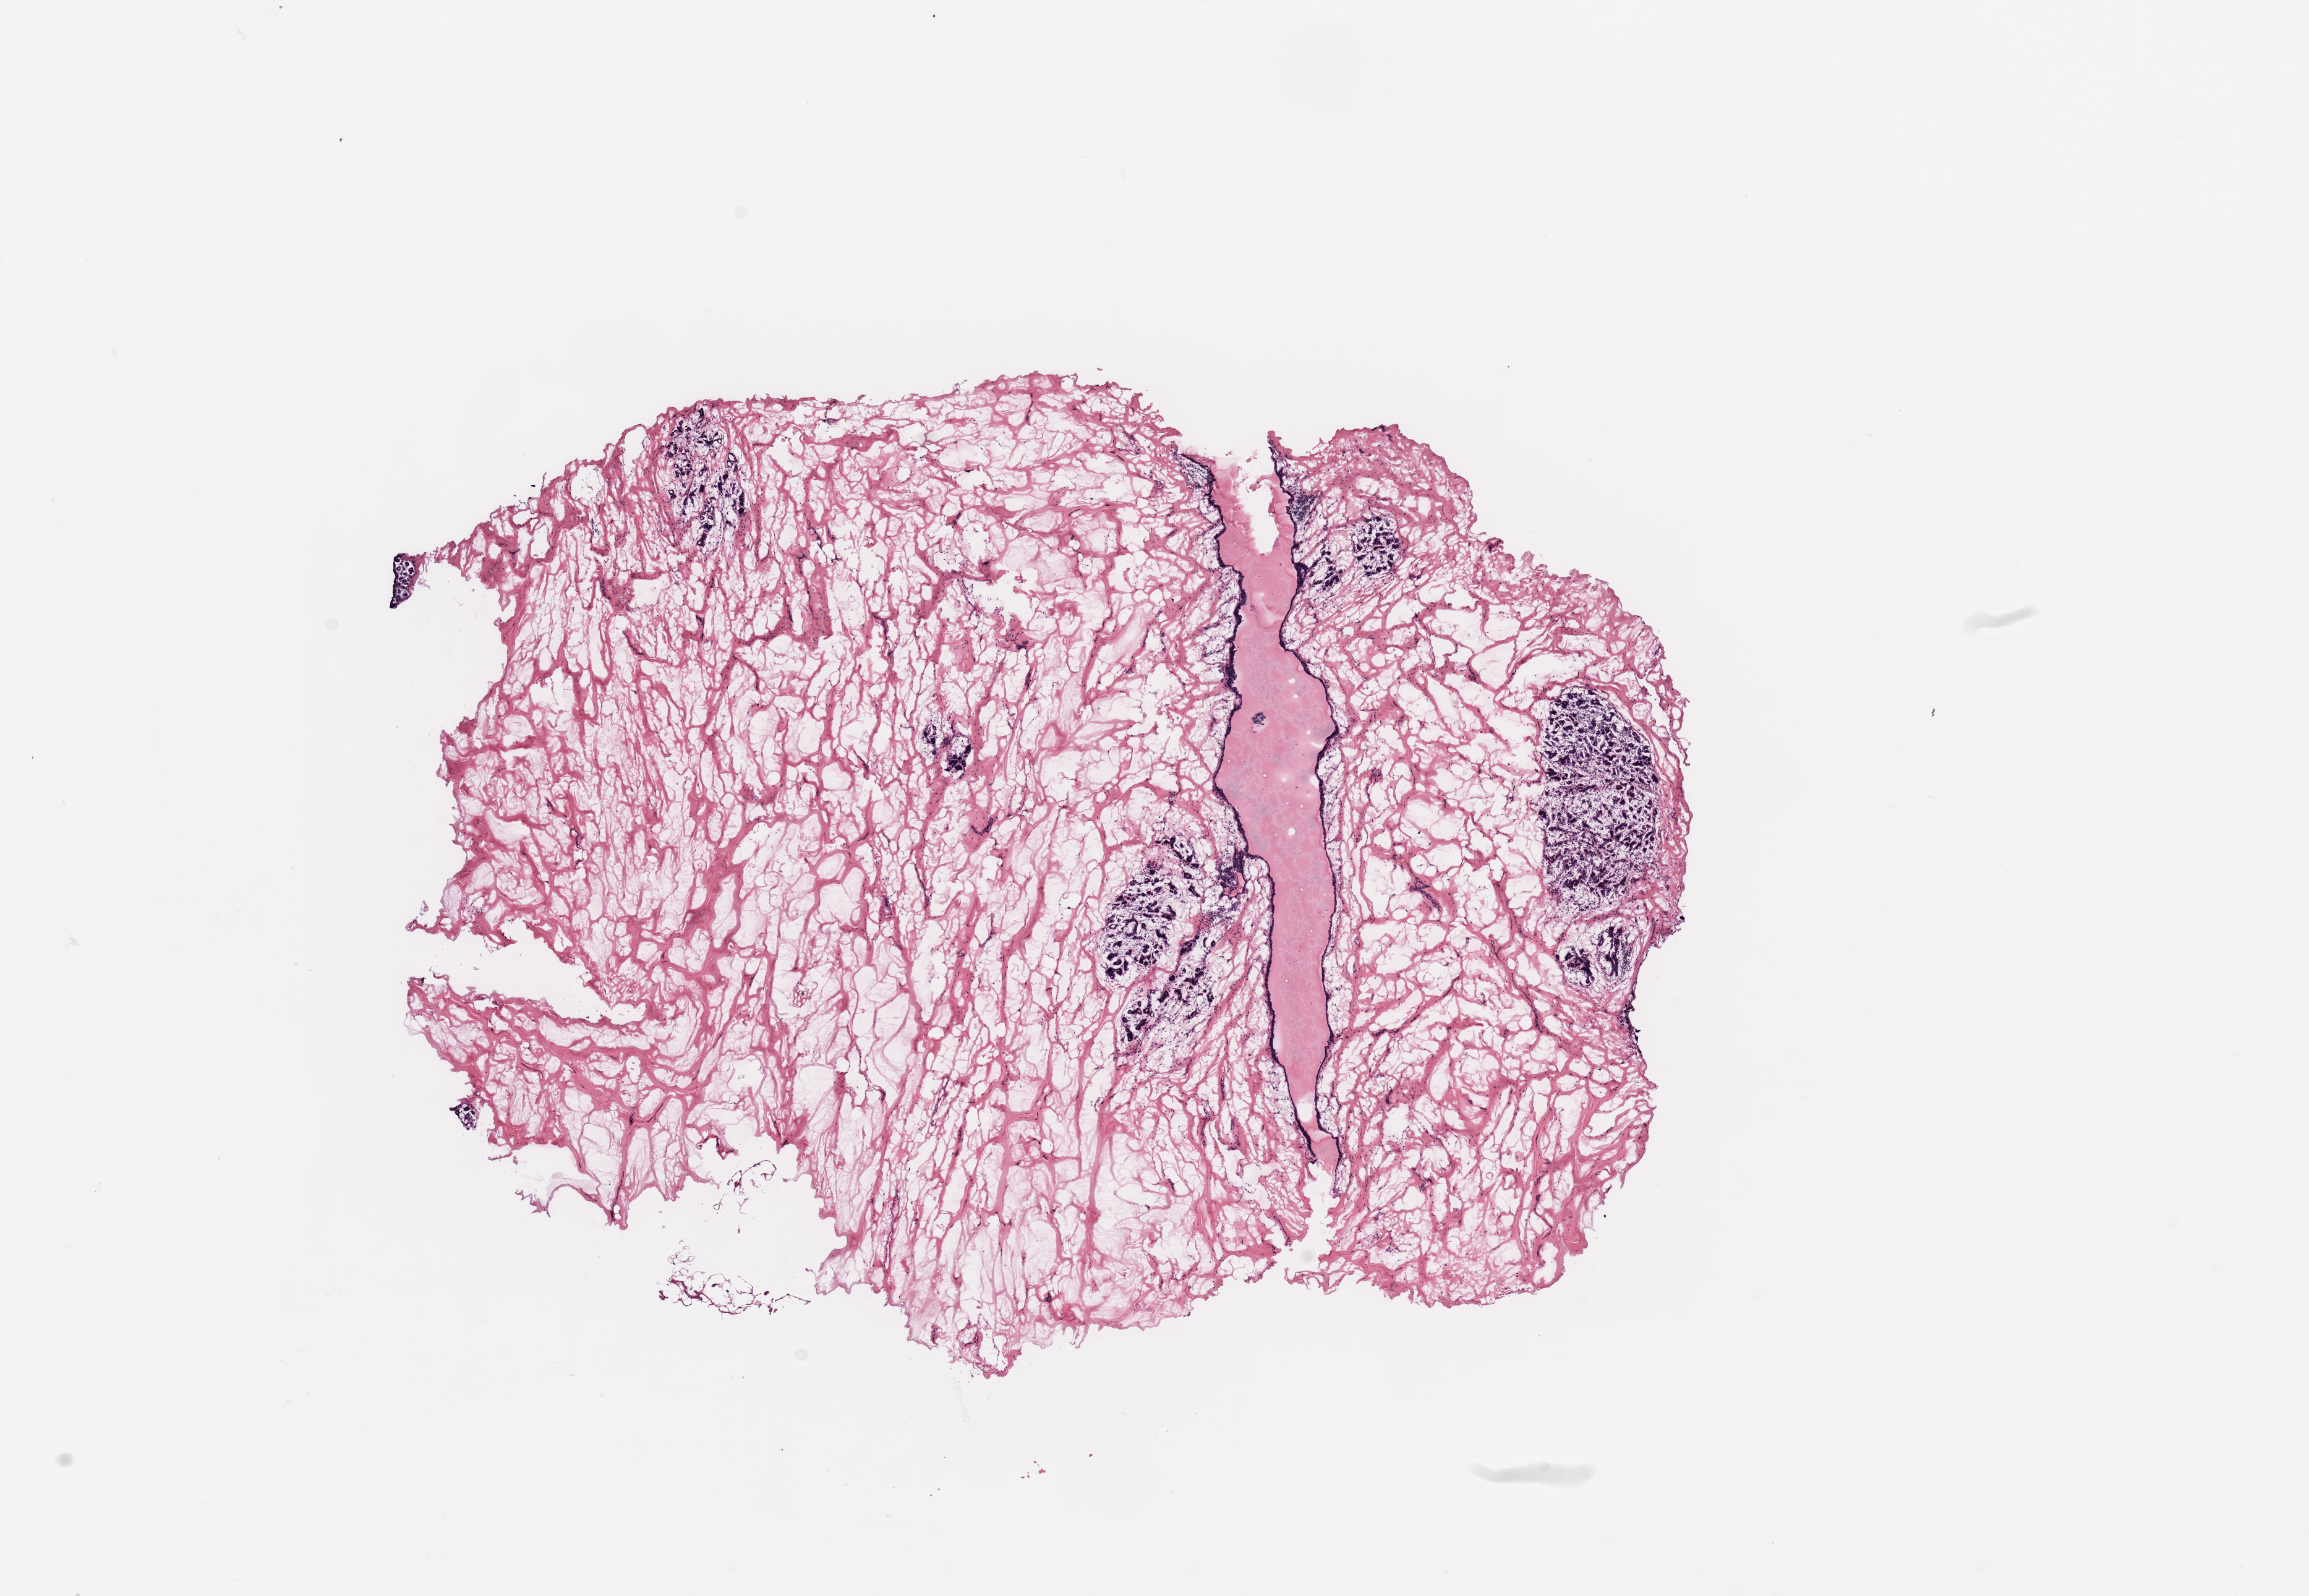
Digitized Hematoxylin and eosin (H&E) stained tissue section (whole slide) — a low-resolution overview of the entire scanned area, about 14.8 x 10.2 mm (slide scanned at 20x), breast, tissue type not recorded.
• patient diagnosis (cohort enrolment): breast cancer (breast)